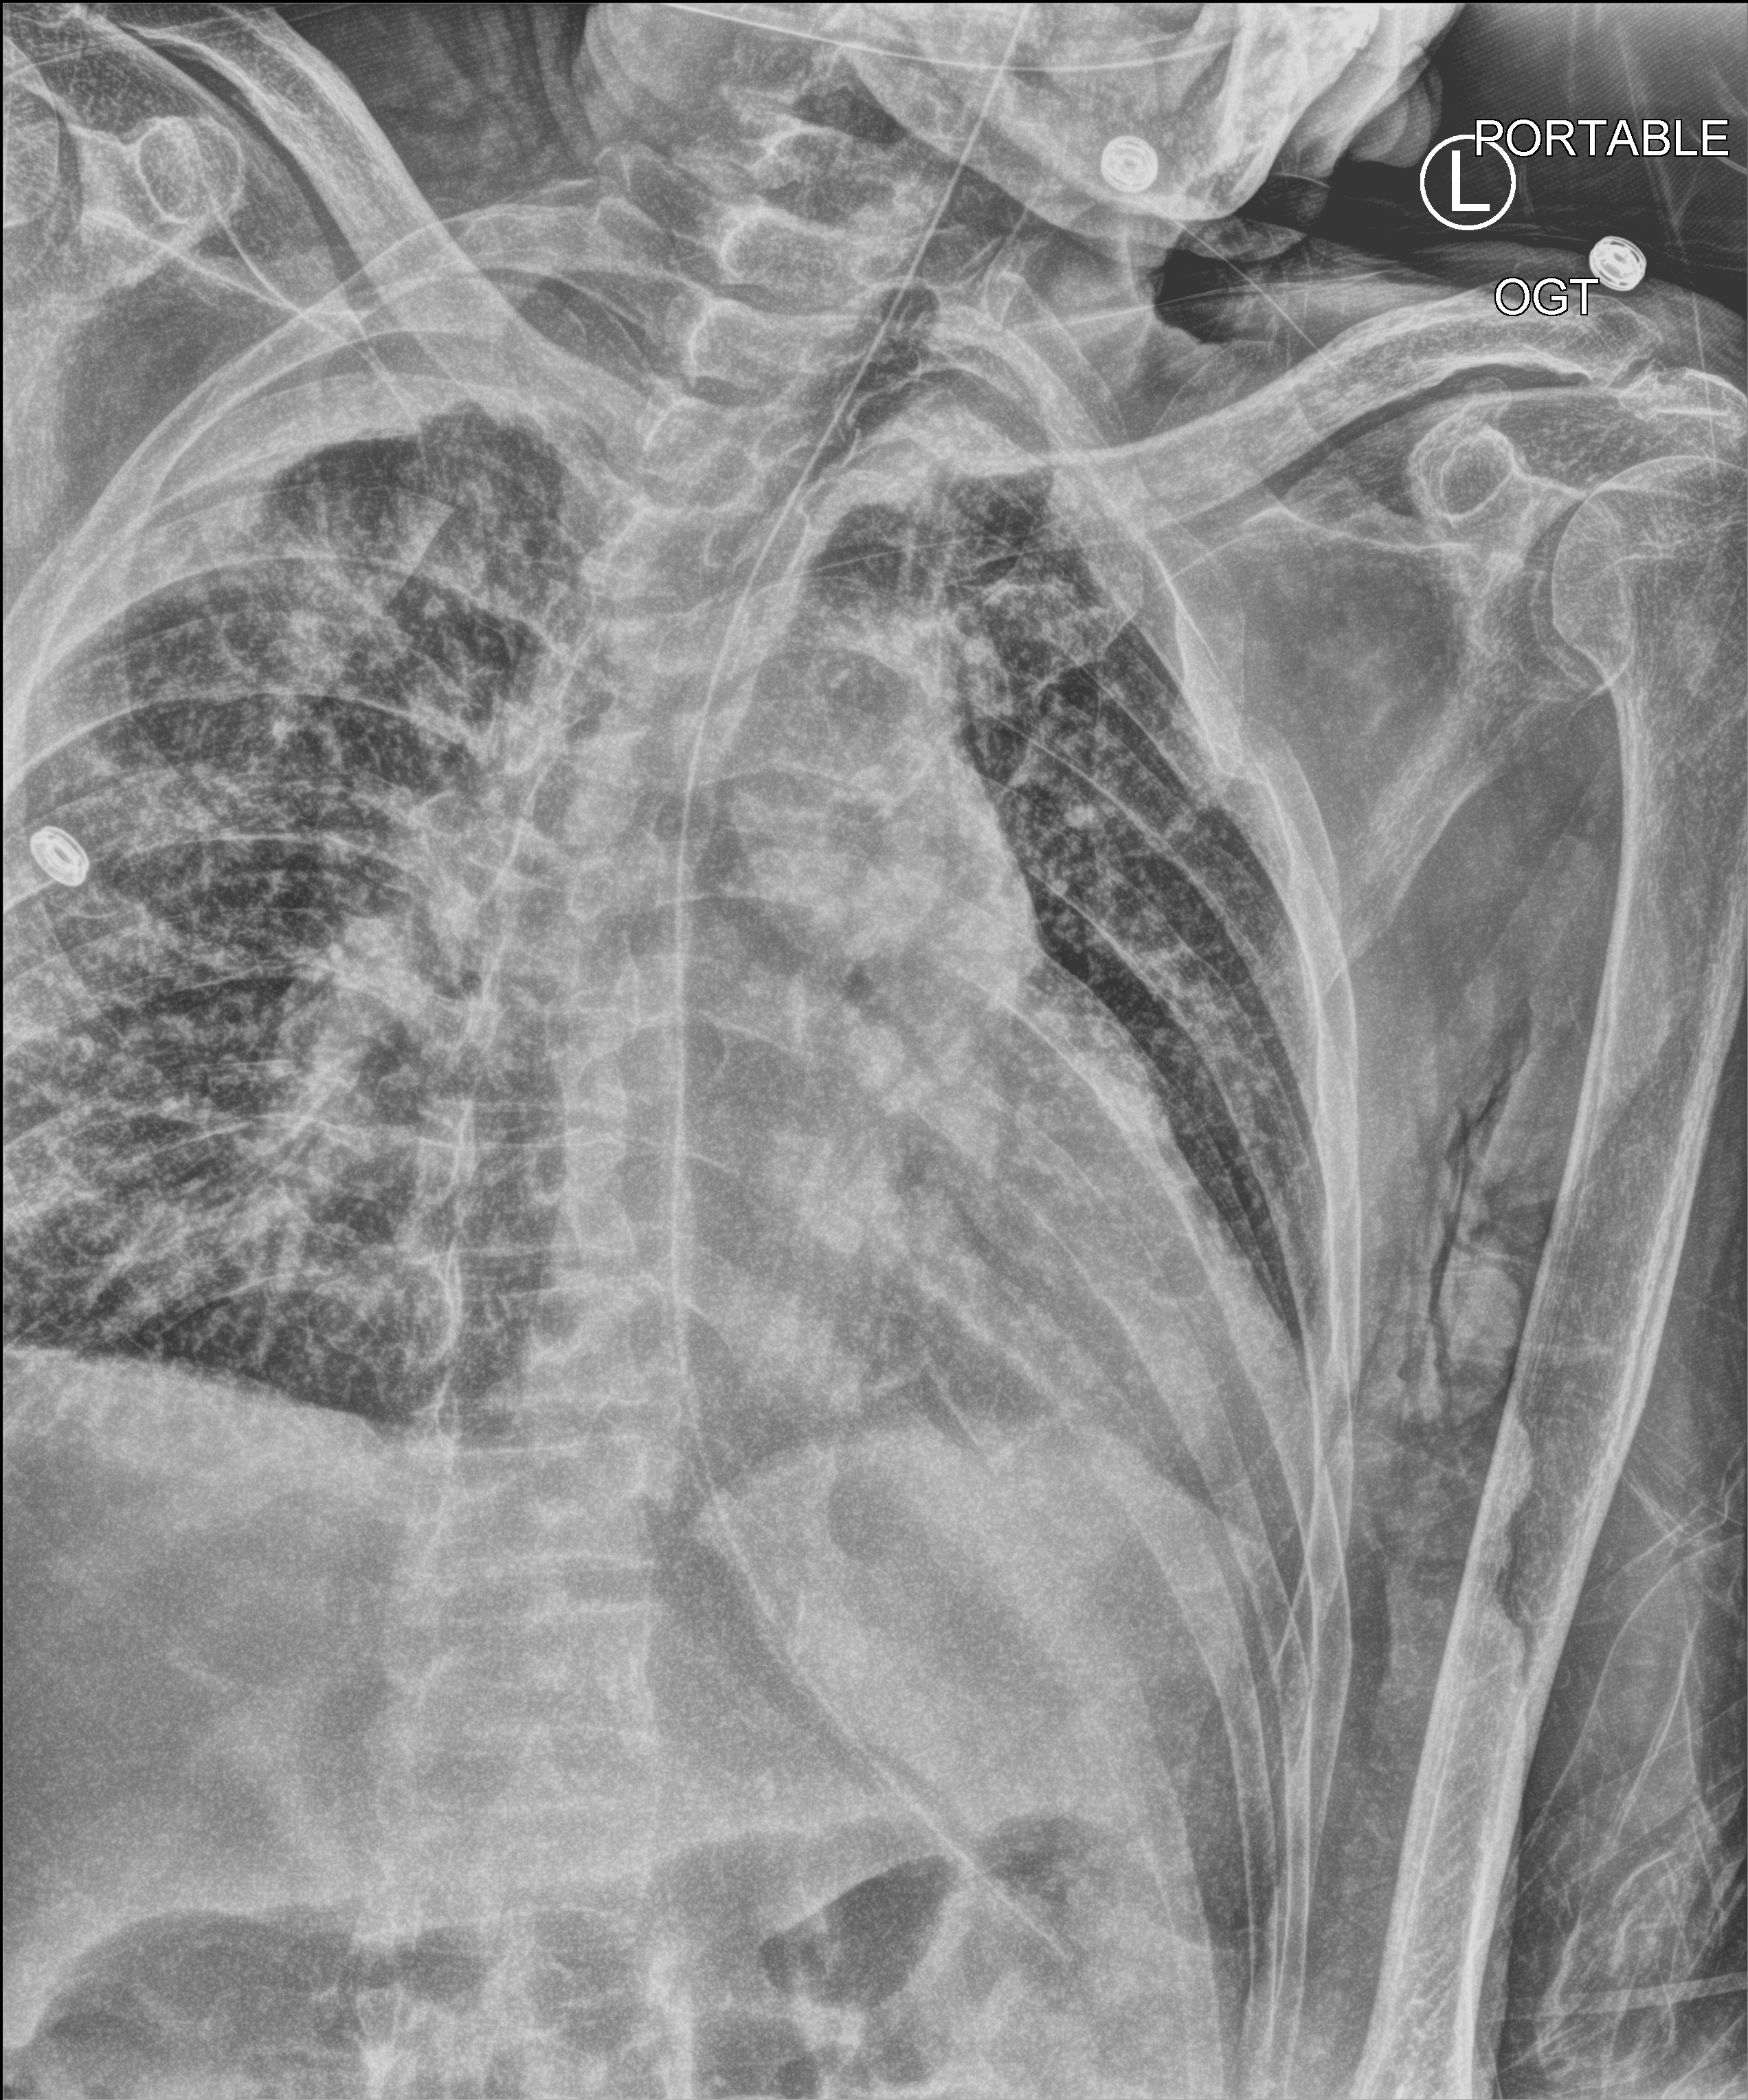
Bedside chest radiograph (computed radiography), anteroposterior (AP) projection. Male patient hospitalised with COVID-19, age 75–90 years.
Hospital-stay facts (about this admission, not read from this image; timing relative to this image not recorded): diabetes (admission record): no; other chronic lung disease (admission record): no; admitted to intensive care during this hospital stay: no.